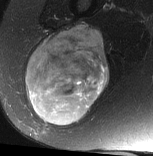
MRI of an extremity soft-tissue mass, one axial slice; T2-weighted fat-saturated; MR volume resampled by the dataset authors to the PET/CT grid (not the native acquisition matrix); 3.27 mm slice thickness; 153 × 156 image matrix. Female patient. Case-level facts recorded for this patient, not image findings: histological type: synovial sarcoma; grade: intermediate; site of the primary tumour: right buttock.
Annotated regions visible in this slice (expert contour drawn on MRI and transferred to this co-registered scan by the dataset authors):
- gross tumour volume including surrounding oedema: bounding box <26,26,109,126> (left, top, right, bottom; pixels)
- gross tumour volume (mass): <26,26,109,126>